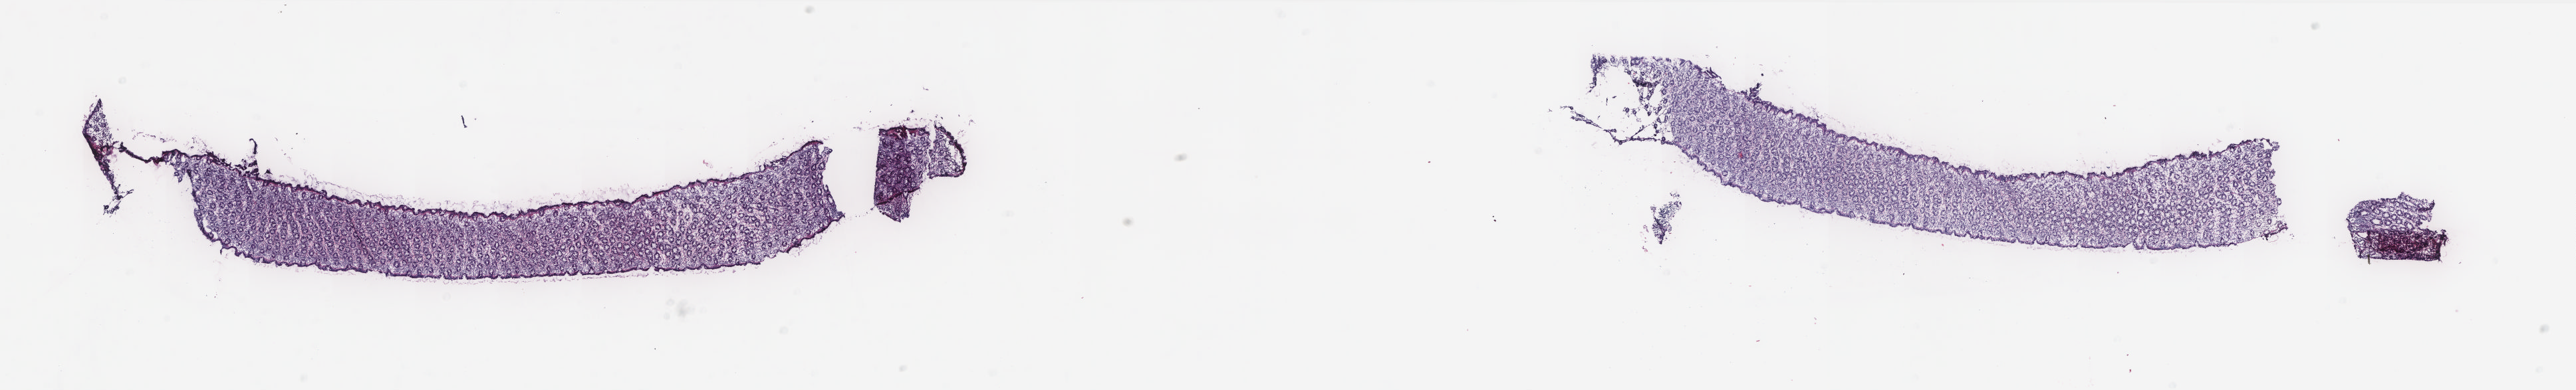
Digitized H&E tissue section (whole slide) — shown as a low-resolution overview of the whole scanned area (about 30.9 x 4.7 mm, acquisition: 20x scan), frozen section, solid tissue normal (non-tumour tissue) sample from the rectum. Male patient; age at initial diagnosis 67 years. Pathologist review of this section (percent, as recorded): tumour cells 0%, normal cells 100%. Infiltration values recorded for this section: lymphocyte infiltration 35%, monocyte infiltration 8%, neutrophil infiltration 0%.
This section: solid tissue normal (non-tumour) sample from the same patient. Patient diagnosis: Adenocarcinoma, NOS.